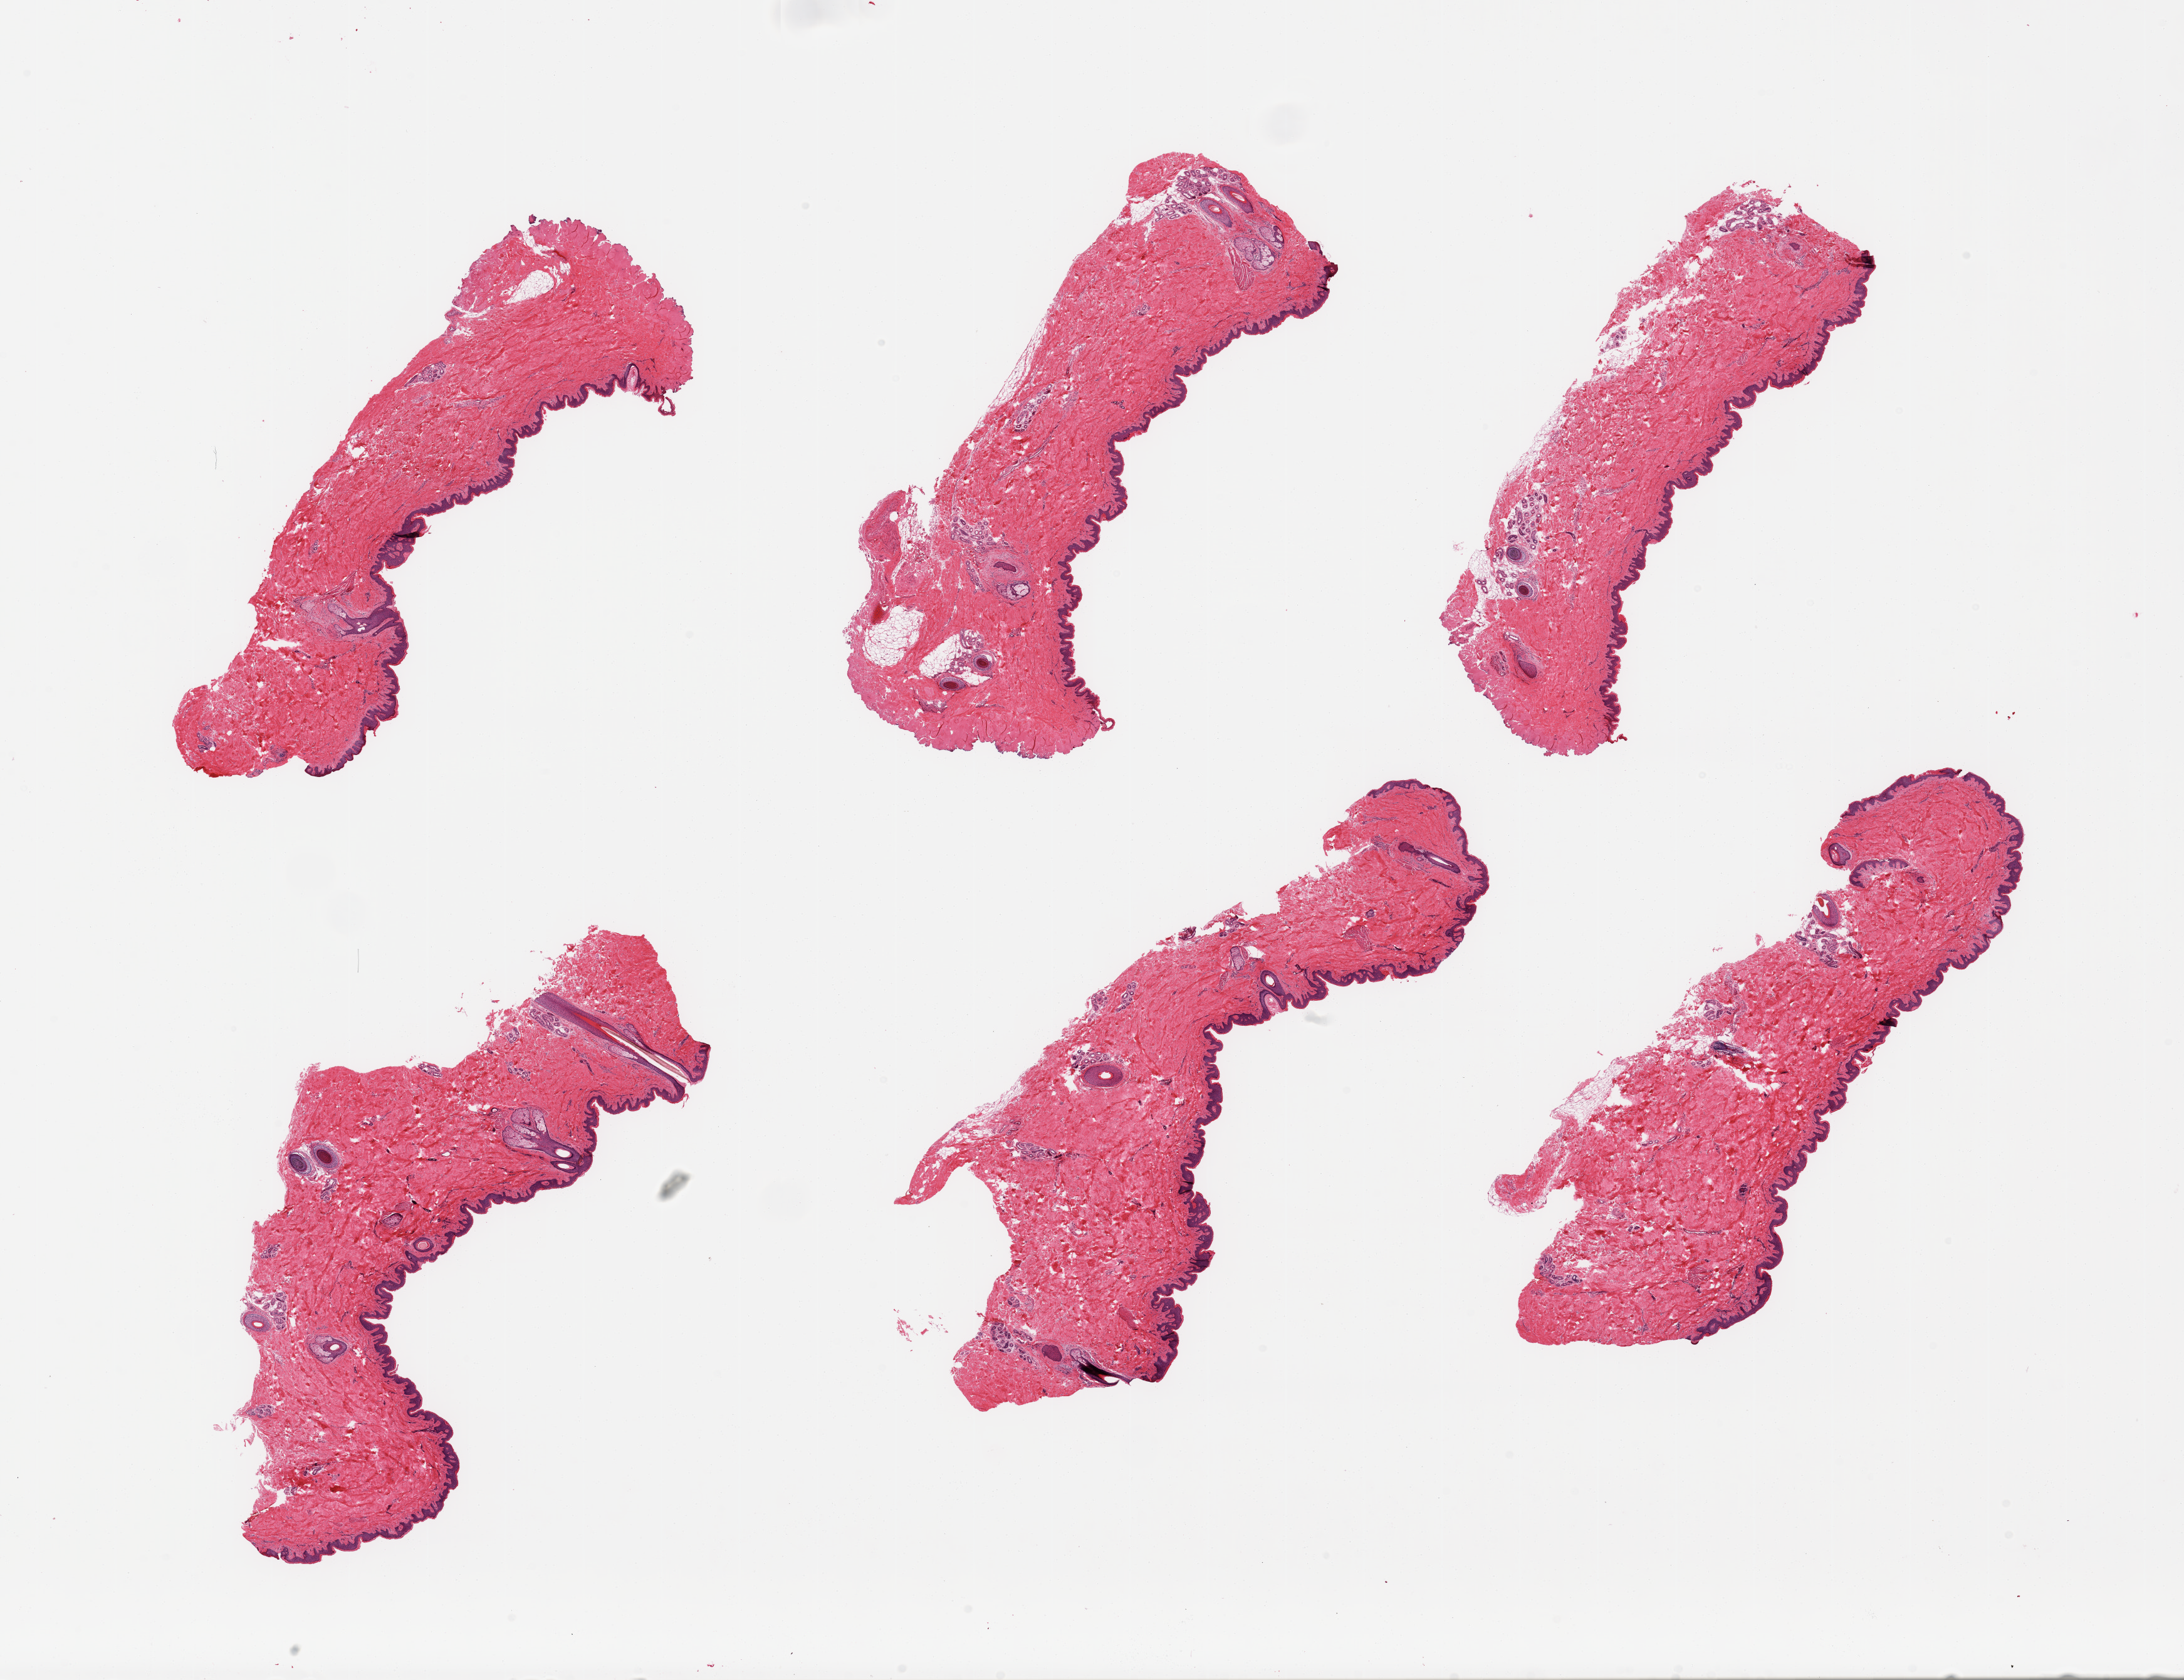
Digitized haematoxylin and eosin-stained section — low-resolution overview of the scanned area, about 27.6 x 21.2 mm (slide scanned at 20x). PAXgene-fixed, paraffin-embedded tissue. Section of skin of suprapubic region (target tissue). Donor tissue sample. Donor sex: male.
Reviewer comment on this tissue sample: 6 pieces, no dermal fat; squamous epithelium is ~40 microns.